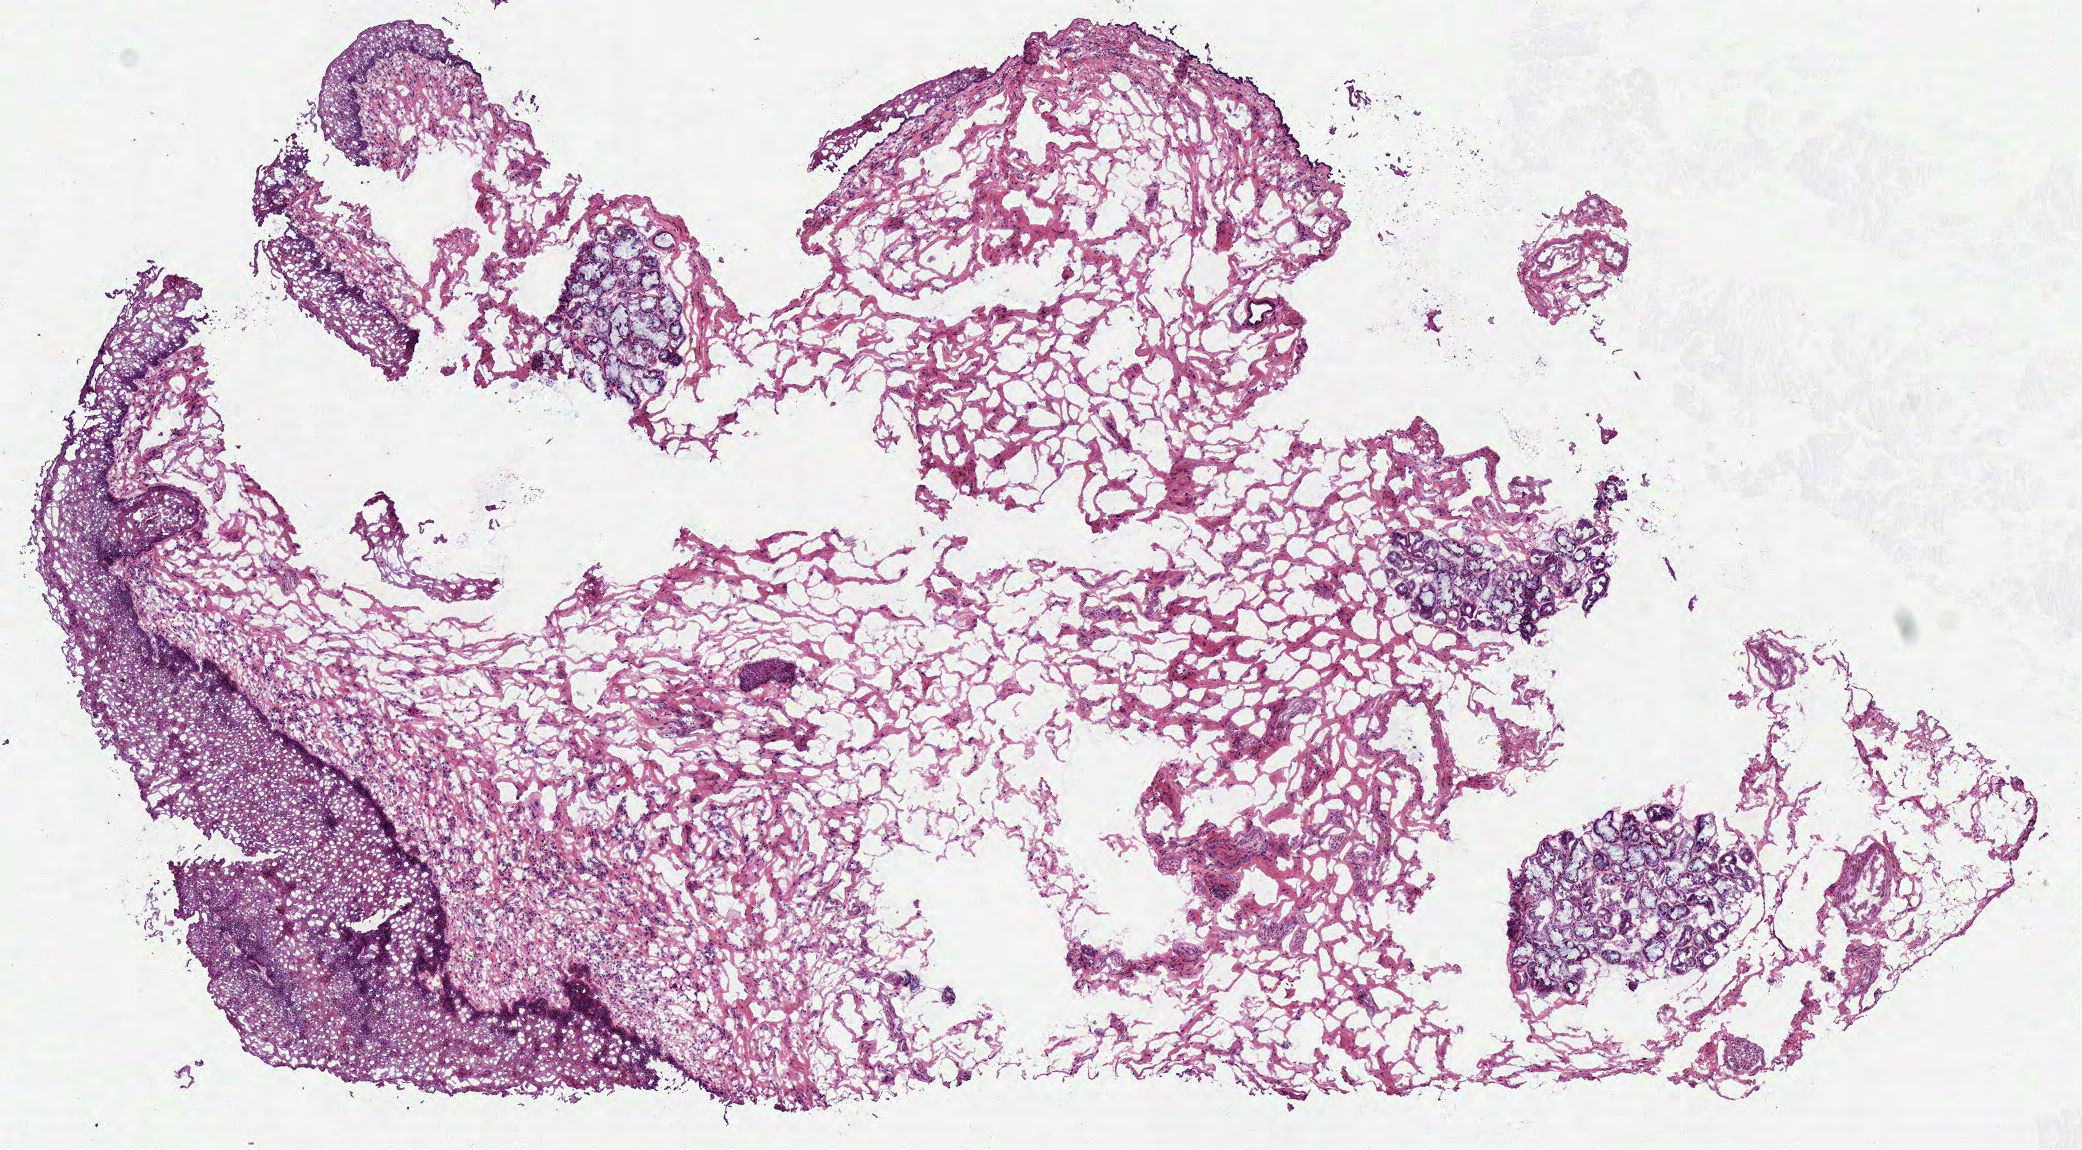
Whole-slide histology image, H&E — shown as a low-resolution overview of the whole scanned area (about 8.2 x 4.5 mm, acquisition: 40x scan); frozen section from the top of the tissue portion; sample: solid tissue normal (non-tumour tissue), head and neck. Female patient; age at initial diagnosis 82 years.
* this section: solid tissue normal sample (biorepository sample class)
* patient diagnosis: Squamous cell carcinoma, NOS (larynx, NOS)